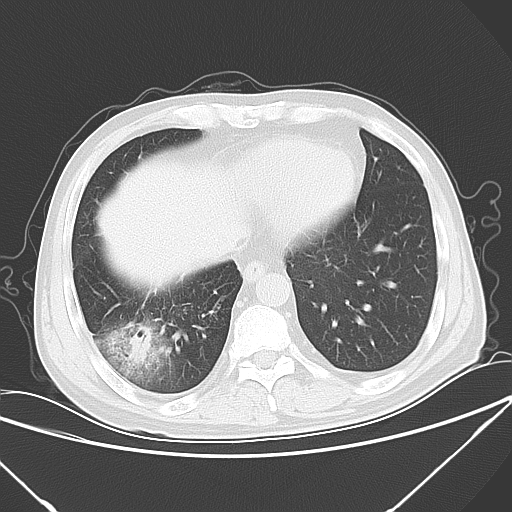
Chest CT, one axial slice. Position 19 of 57 along the scan axis. 120 kVp. Lung window (W 1500 / L -600 HU). 5 mm slice thickness. 512 × 512 image matrix. Patient: male, 54 years. Case-level facts recorded for this patient, not image findings: clinical TNM (as recorded): T2 N1 M0.
Outlined on this slice (rectangle marked by the reading radiologist):
- lung tumour (recorded histology: adenocarcinoma): bounding box [x1, y1, x2, y2] px = [129, 325, 153, 361]